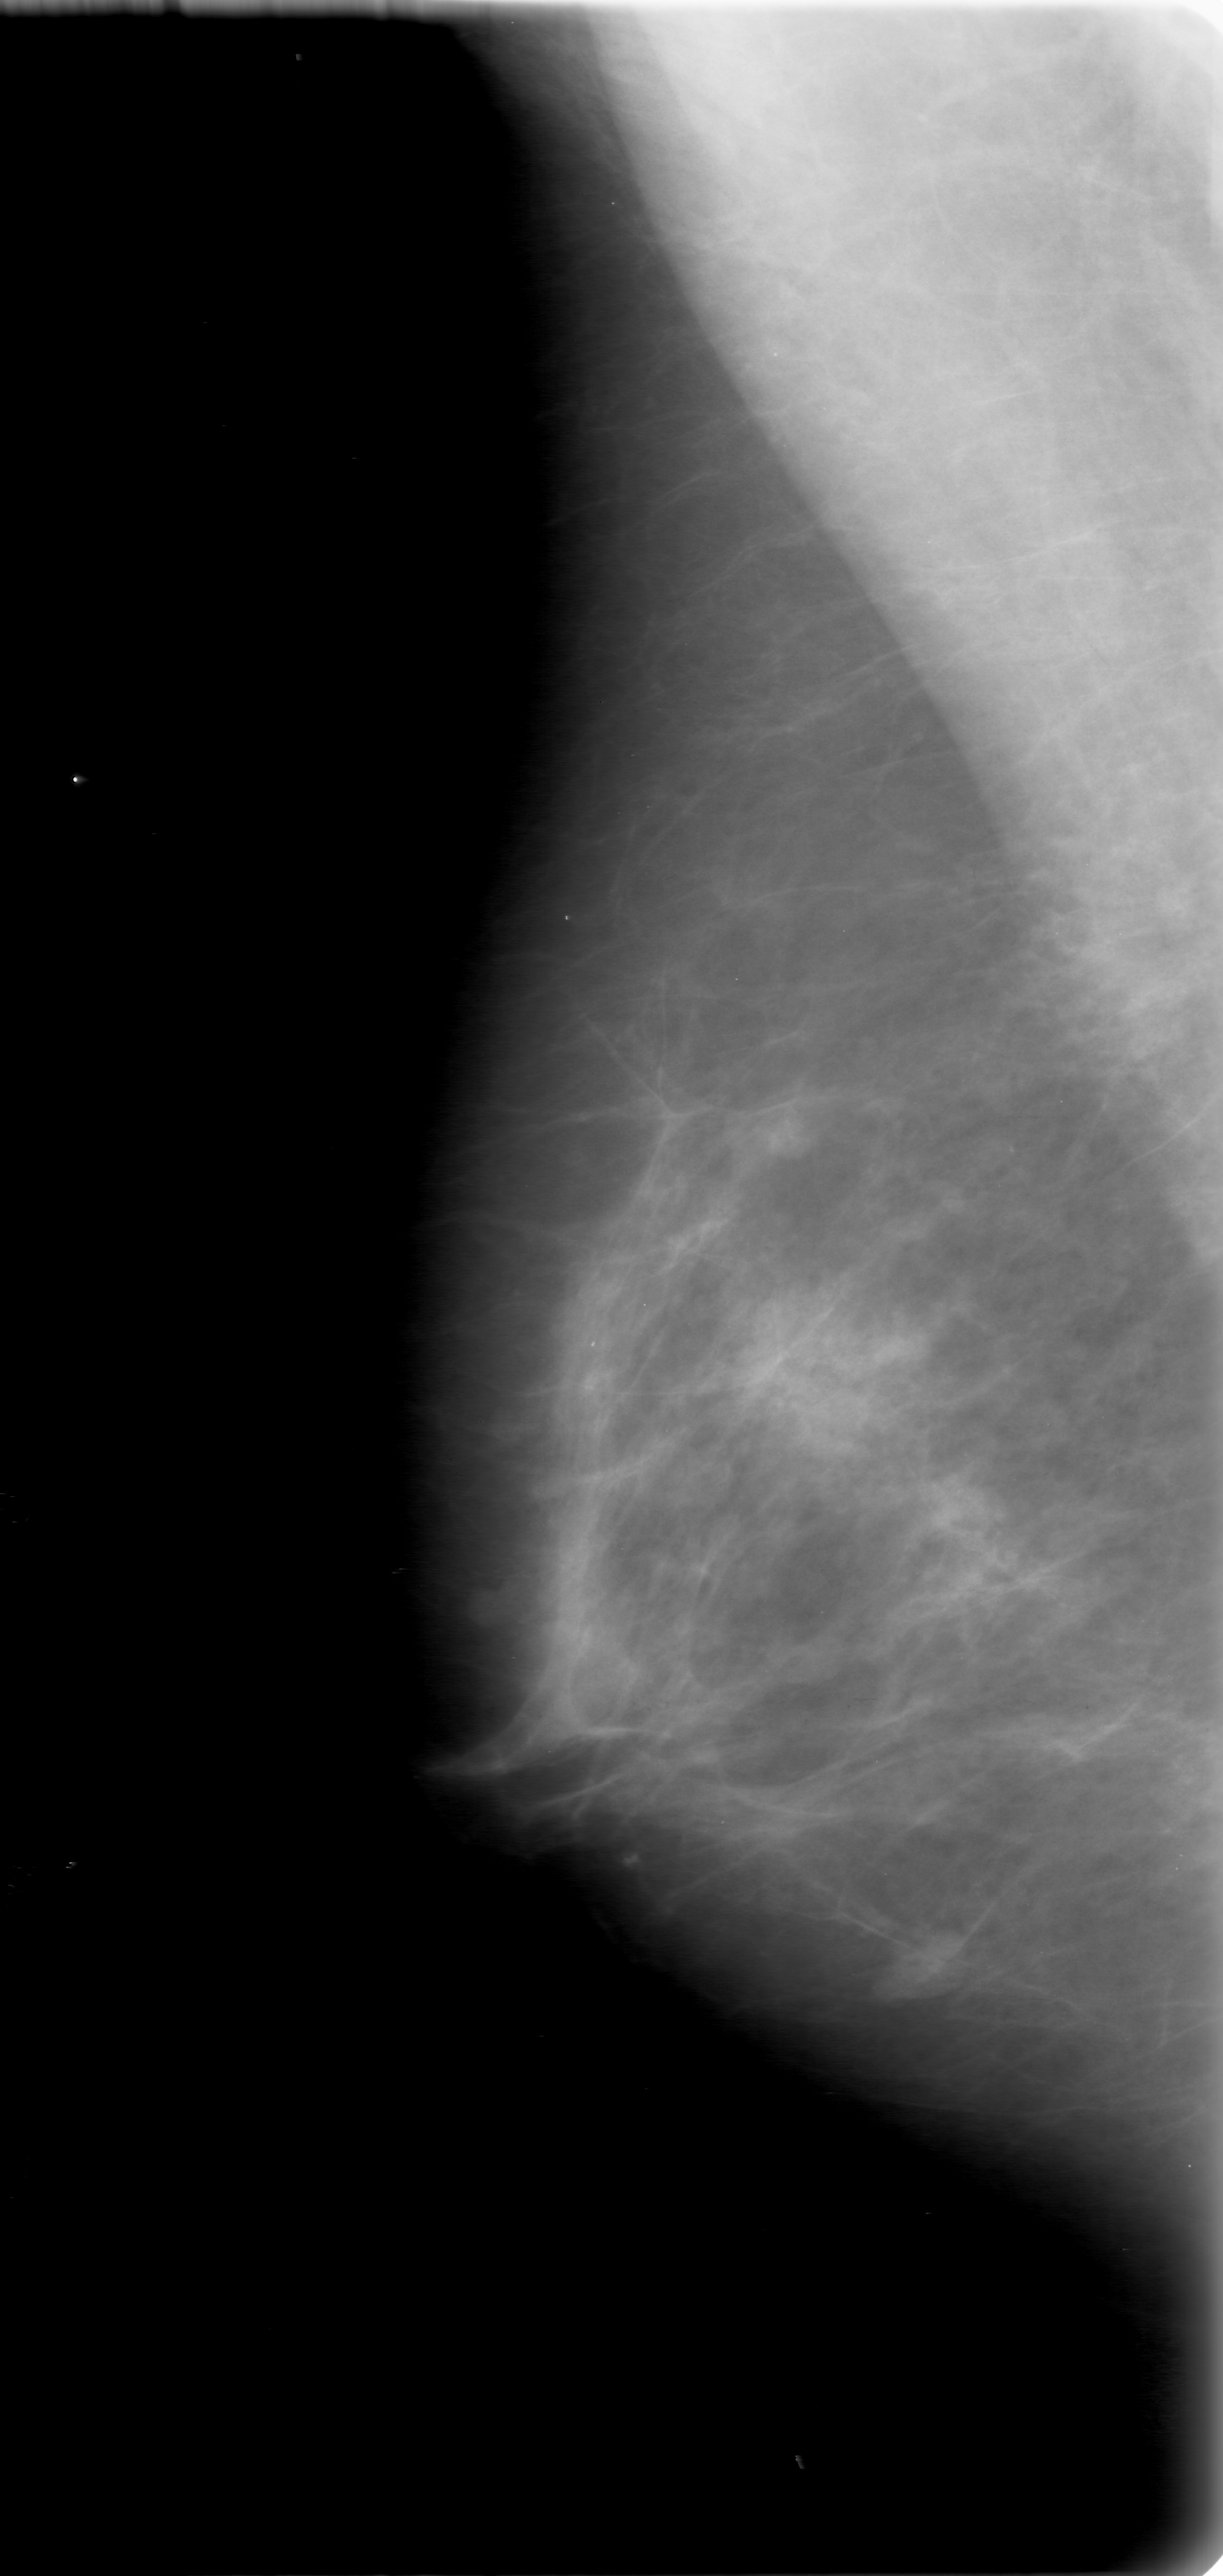
Mammogram (digitized film). Right breast. MLO view. BI-RADS breast density category 2 (scale 1–4). 1223 × 2576 image matrix.
Expert-marked regions of interest on this image (one box per marked abnormality):
- mass, shape oval, margins obscured; BI-RADS assessment category 0 (incomplete: needs additional imaging); pathology (as recorded): benign: bounding box (x1, y1, x2, y2) in pixels: (850, 1906, 992, 2023)